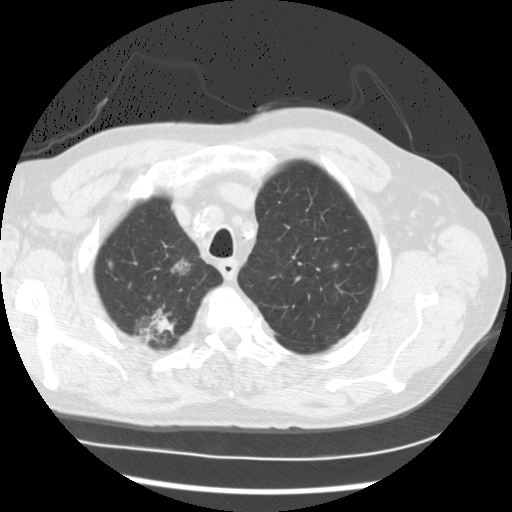
Chest CT (low-dose screening protocol), one axial image, baseline screening round, lung window (W 1500 / L -600 HU). Male participant, aged 68 years at enrolment. Current smoker at enrolment.
Expert reader's lesion annotation, box from (x=115, y=290) to (x=191, y=360) px. The screening reader recorded 3 non-calcified nodules or masses ≥4 mm on this exam (right upper lobe, right upper lobe, right lower lobe); which of them this box marks is not recorded.